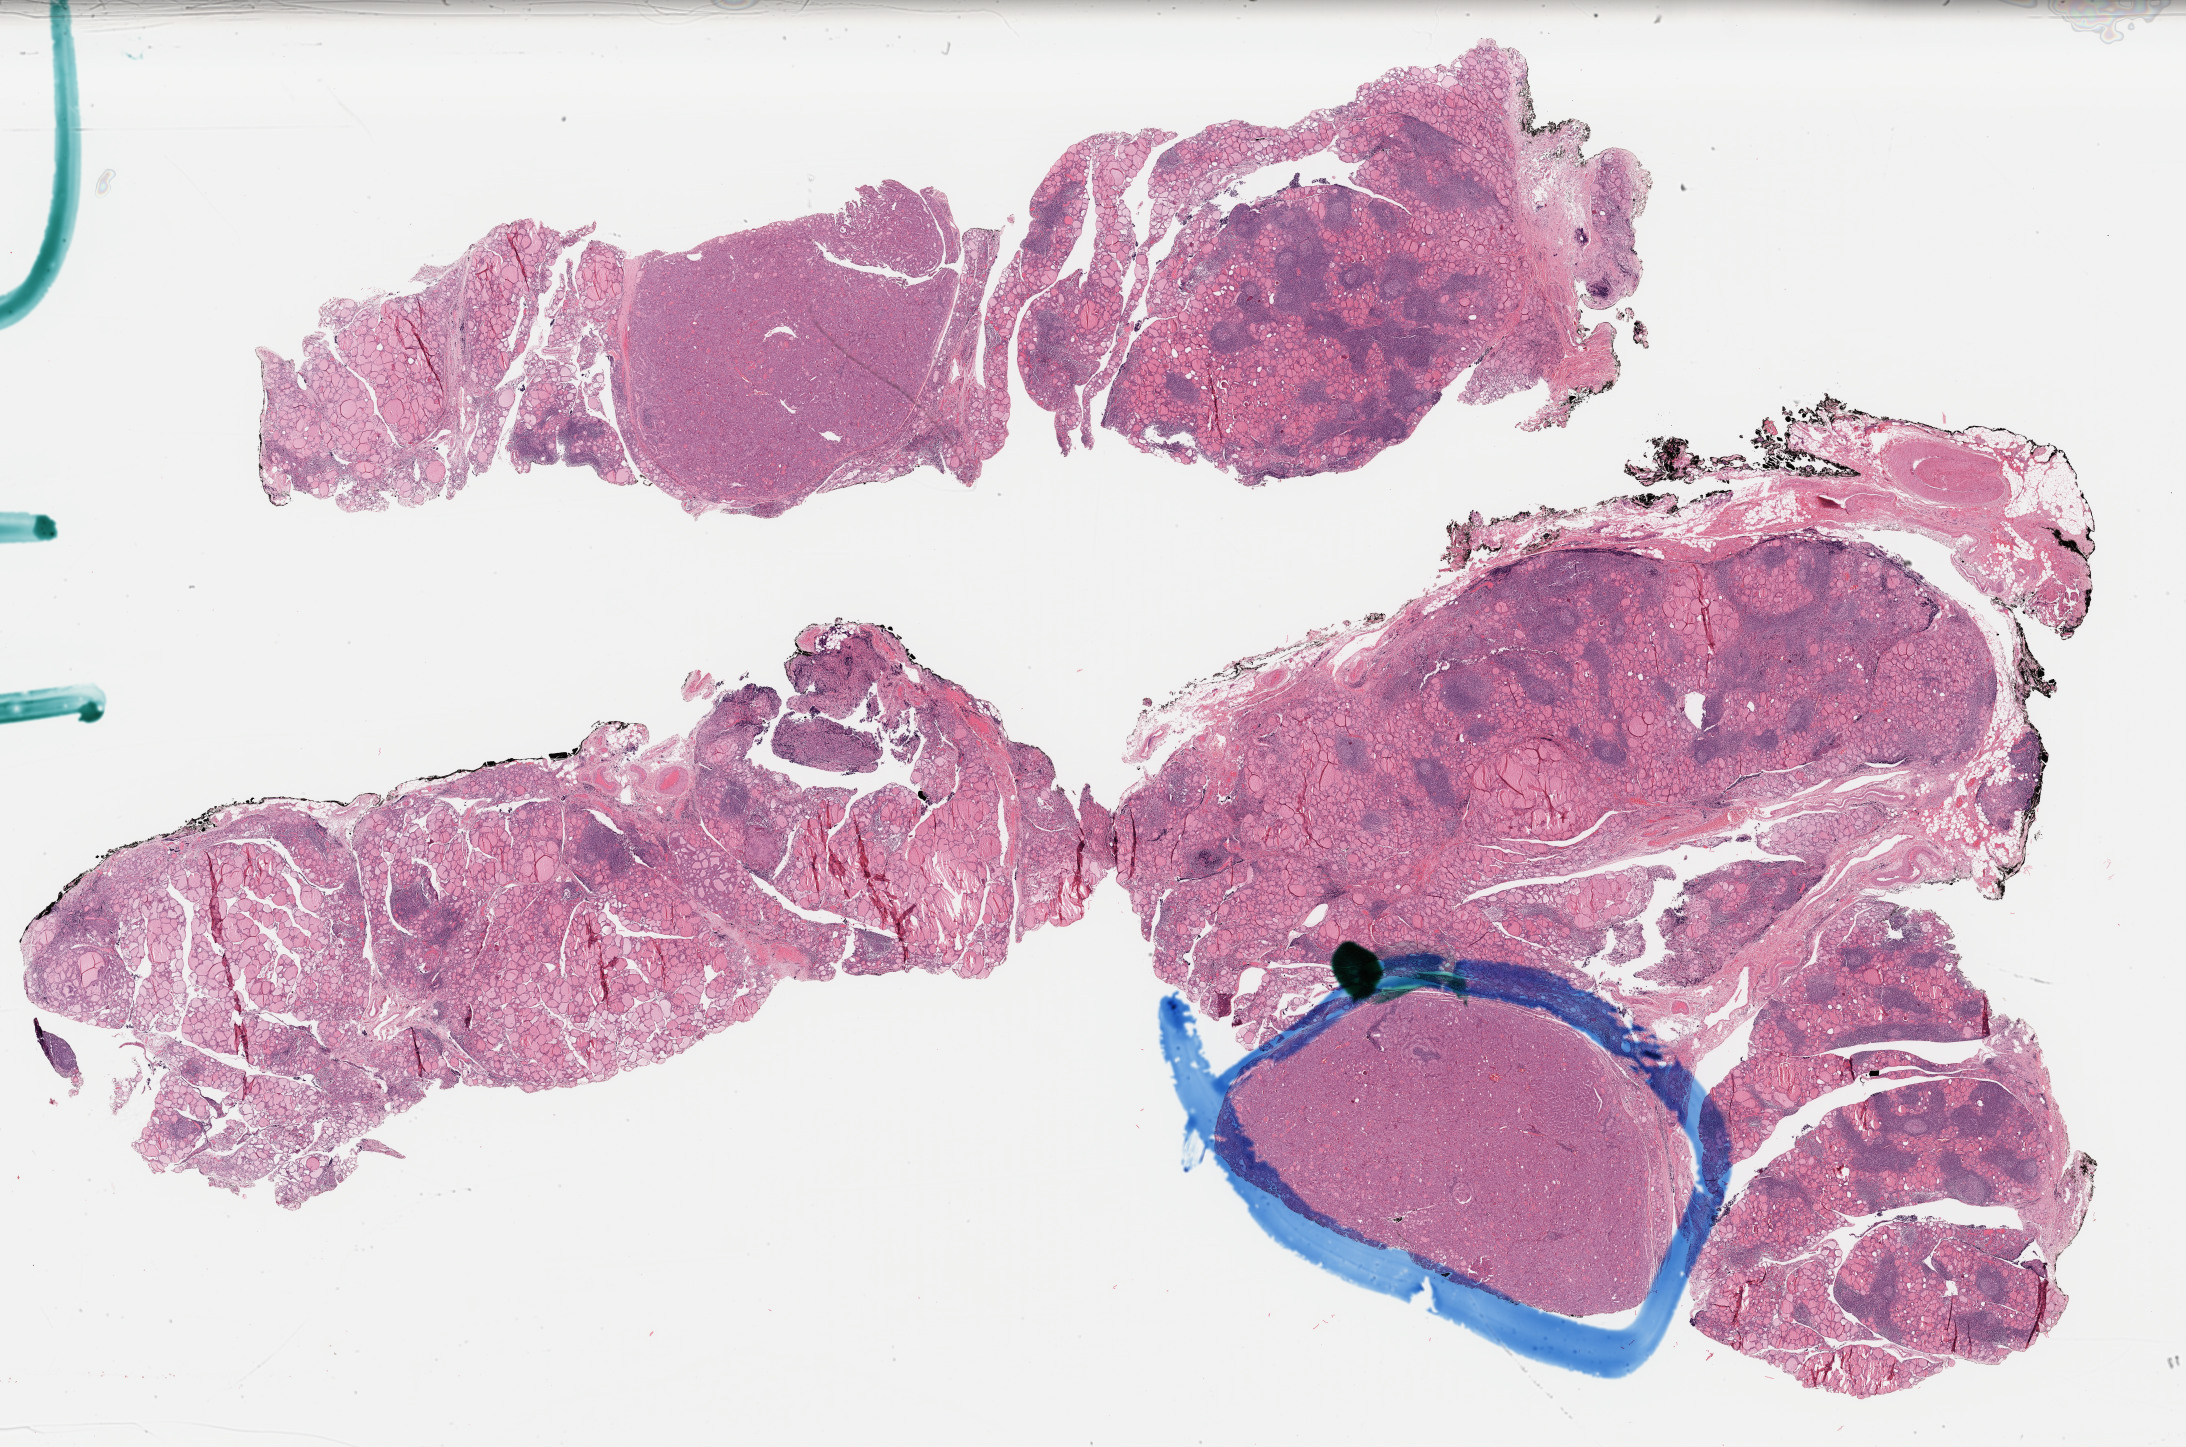
Hematoxylin and eosin (H&E) stained whole-slide image — shown as a low-resolution overview of the whole scanned area (about 34.5 x 22.9 mm). Formalin-fixed paraffin-embedded (FFPE) diagnostic section. Primary tumour sample from the thyroid. Female patient; age at initial diagnosis 47 years.
AJCC pathologic stage: I. Diagnosis: Papillary carcinoma, follicular variant.